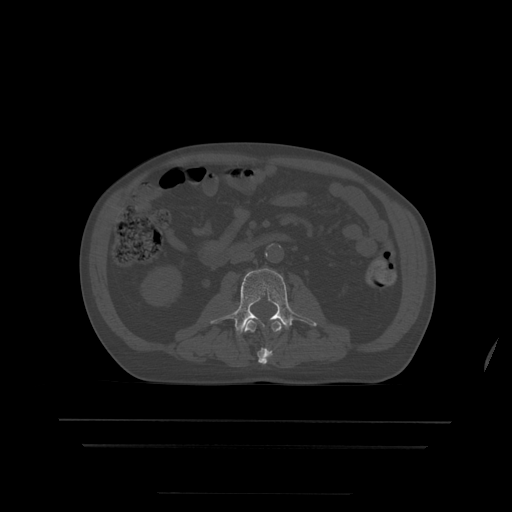
CT including the spine, one axial slice. Slice 125 of 522 in the series (ordered by position). Bone window (W 1800 / L 400 HU). 512 × 512 image matrix, field of view 436 × 436 mm. Patient age 68 years. From the clinical record (not read from this slice): primary cancer: urothelial.
Outlined on this slice (semi-automatic segmentation, software-assisted and operator-edited):
- L2 vertebra: box from (x=244, y=321) to (x=282, y=365) px
- L3 vertebra: (x=211, y=269)–(x=317, y=335)